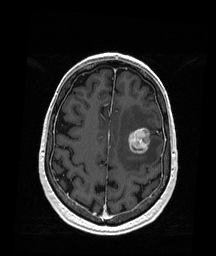
Brain MRI from a brain-tumour surgery series, one axial slice. Slice 57 of 176 in the series (ordered by position). T1-weighted post-contrast. 1 mm slice thickness. 216 × 256 image matrix. Case-level facts recorded for this patient, not image findings: histopathology: Metastatic Melanoma; tumour location: Left Frontal.
Outlined on this slice (expert manual segmentation):
- tumour: box from (x=128, y=128) to (x=151, y=154) px